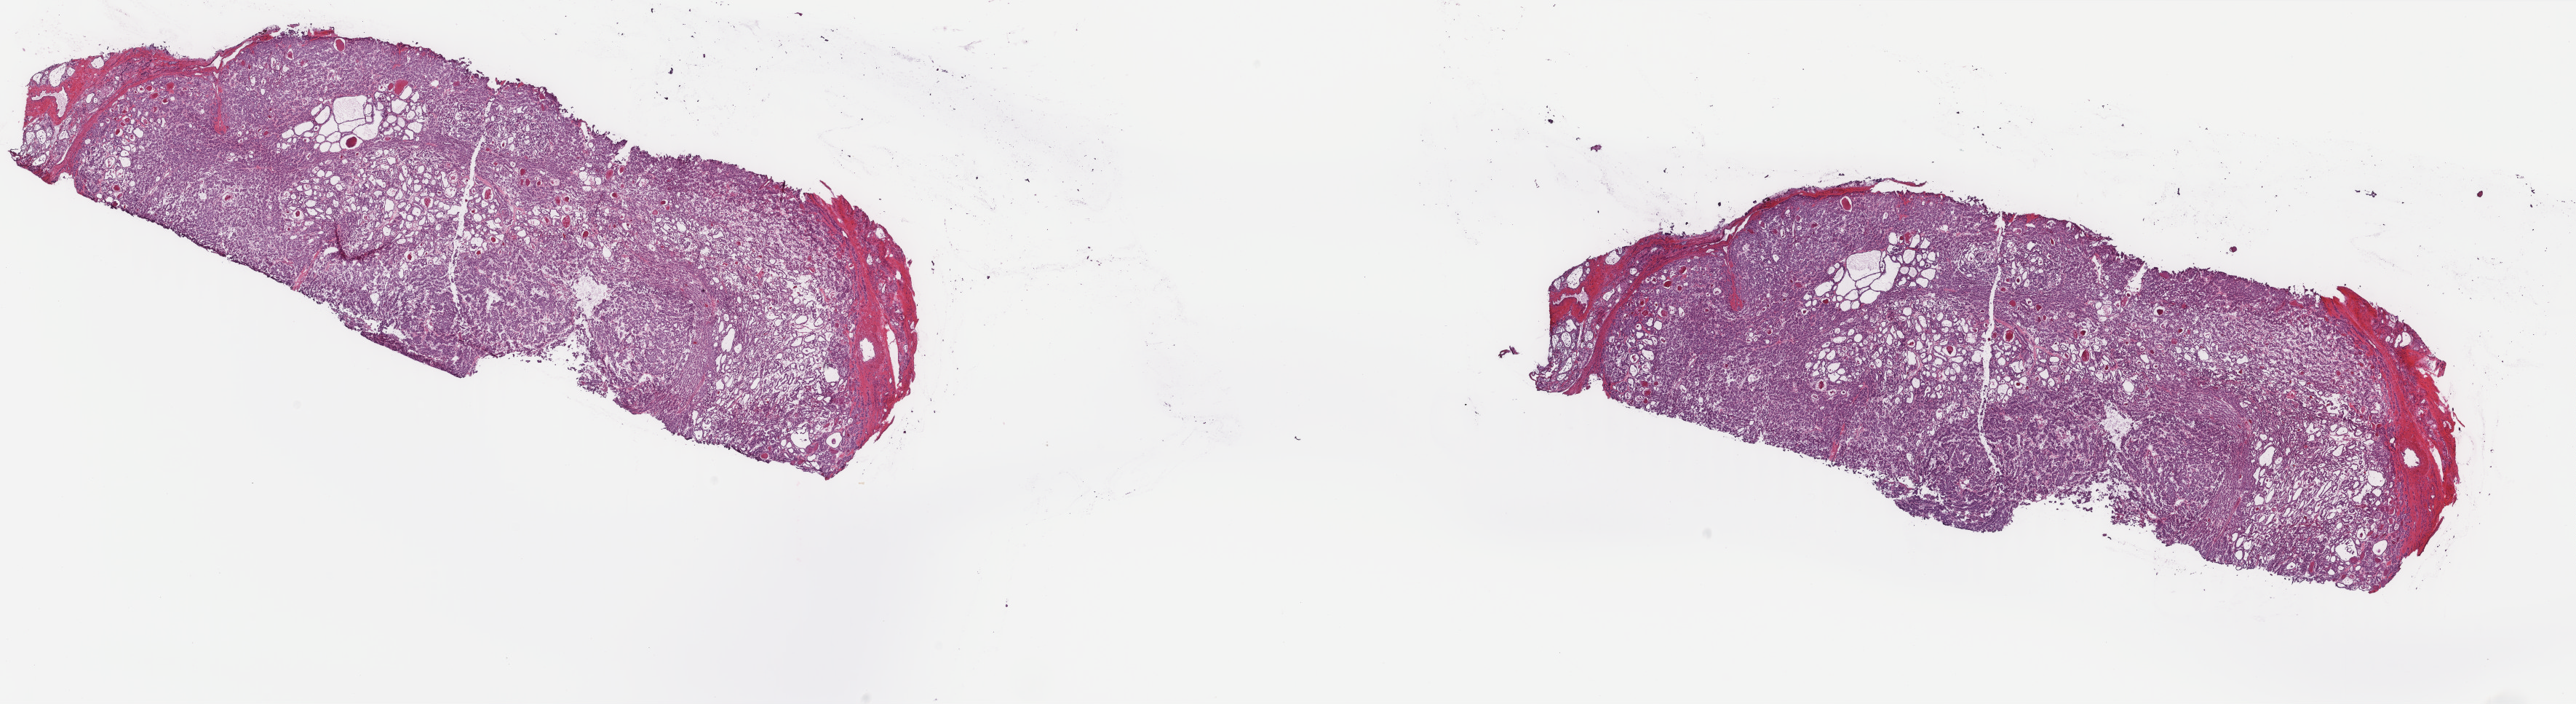
Whole-slide histology image, Hematoxylin and eosin (H&E) stained, a low-resolution overview of the entire scanned area, about 28.1 x 7.7 mm, frozen section from the top of the tissue portion, primary tumour sample from the thyroid. Male patient; age at initial diagnosis 63 years. Slide review estimates, as recorded: tumour cells 80%, tumour nuclei 95%, normal cells 5%, stromal cells 15%, necrosis 0%. Inflammatory infiltration, as recorded: lymphocyte infiltration 0%, monocyte infiltration 0%, neutrophil infiltration 0%.
- lymph nodes positive (case pathology): 0 of 2 examined
- AJCC pathologic stage: III
- diagnosis: Papillary carcinoma, follicular variant (thyroid gland)